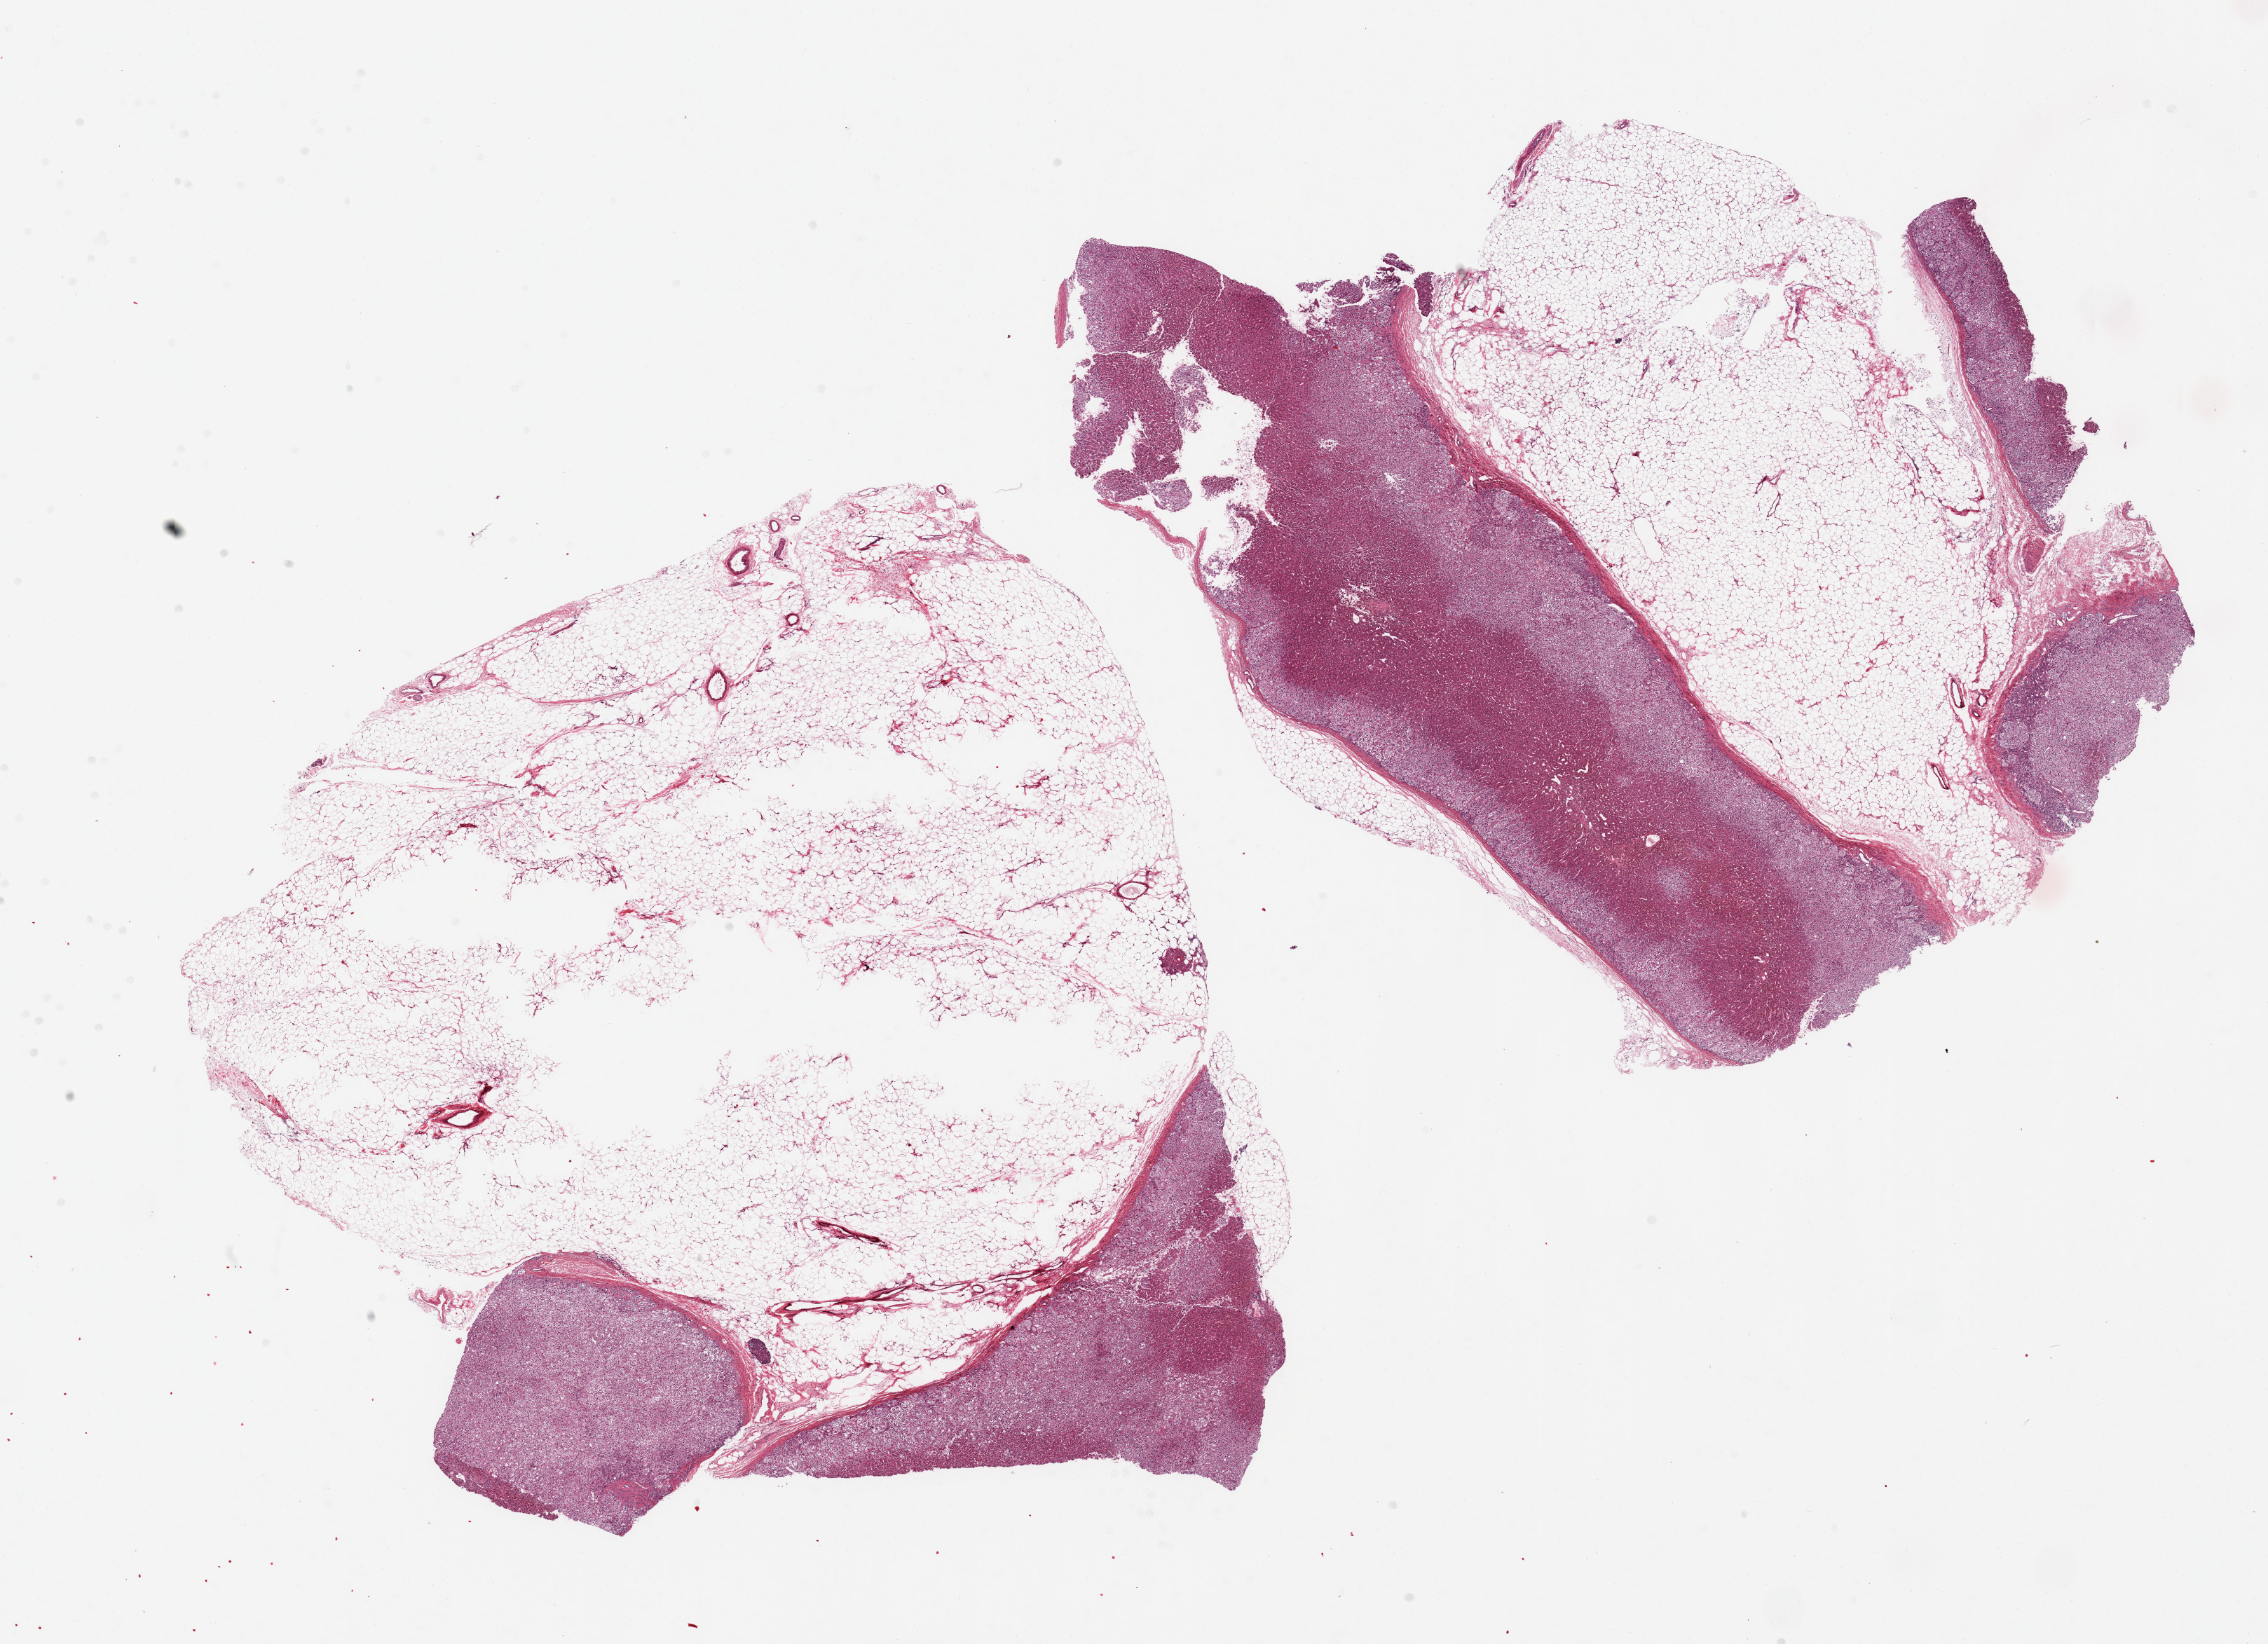
Whole-slide image, haematoxylin and eosin stain, low-resolution overview of the scanned area, about 25.6 x 18.6 mm. PAXgene-fixed, paraffin-embedded tissue. Sampled site (target tissue): adrenal gland. Tissue donor sample. Male donor.
- reviewer comment on this tissue sample: 2 pieces; one with 80% and other with 40% of external fat; adrenal cortex